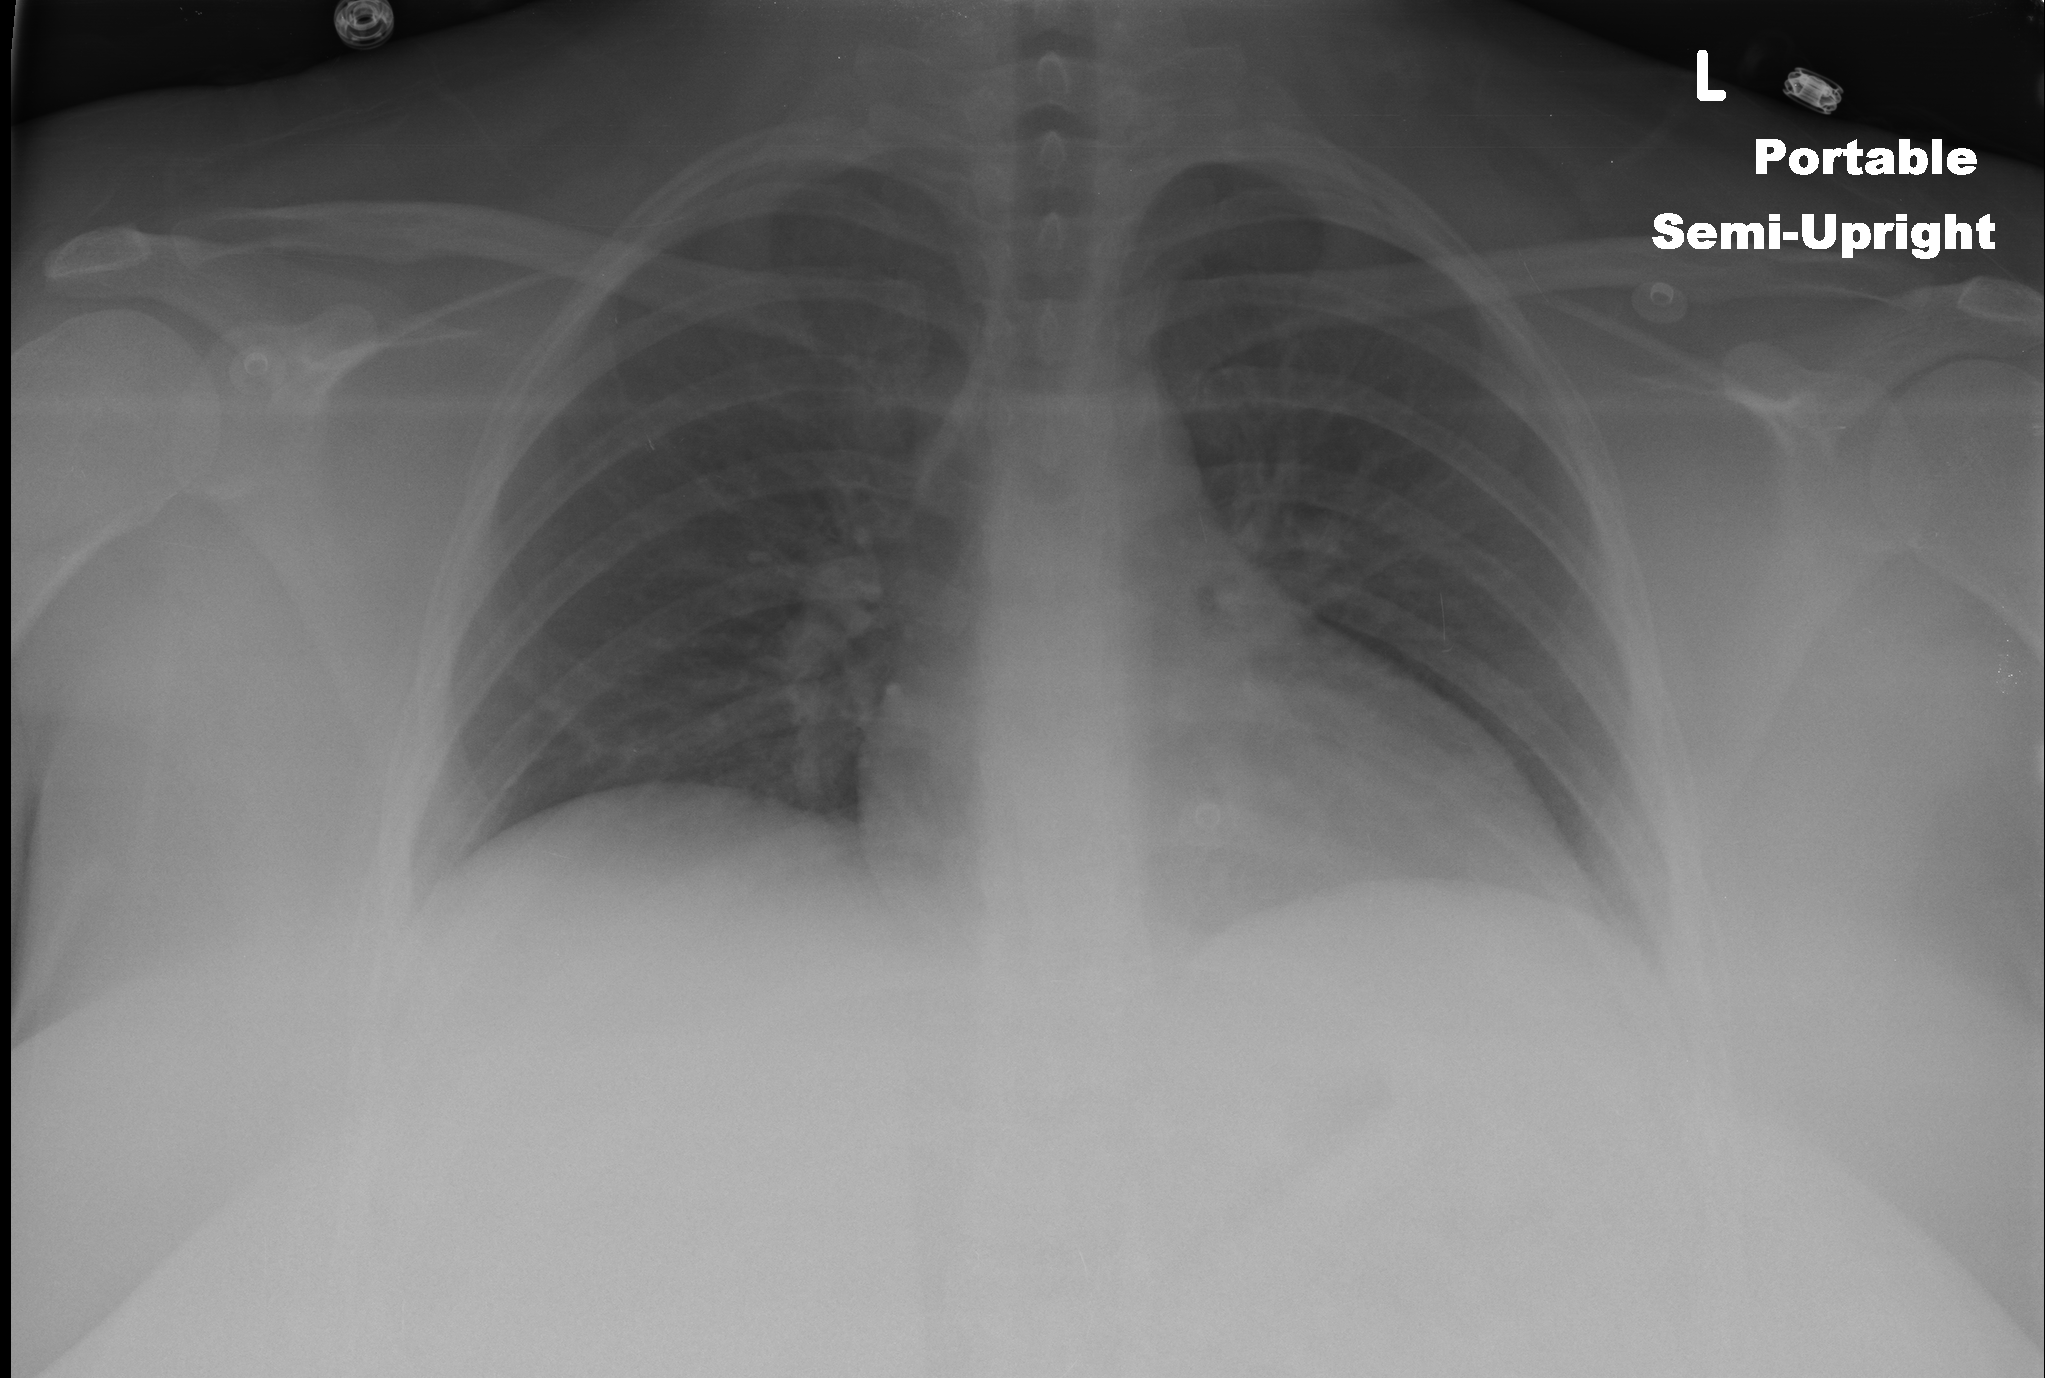
Portable chest radiograph, AP projection. Female patient, age 23 years; imaged 0 days after the COVID-19 diagnosis.
Radiologist key findings (as recorded): The lungs are clear.